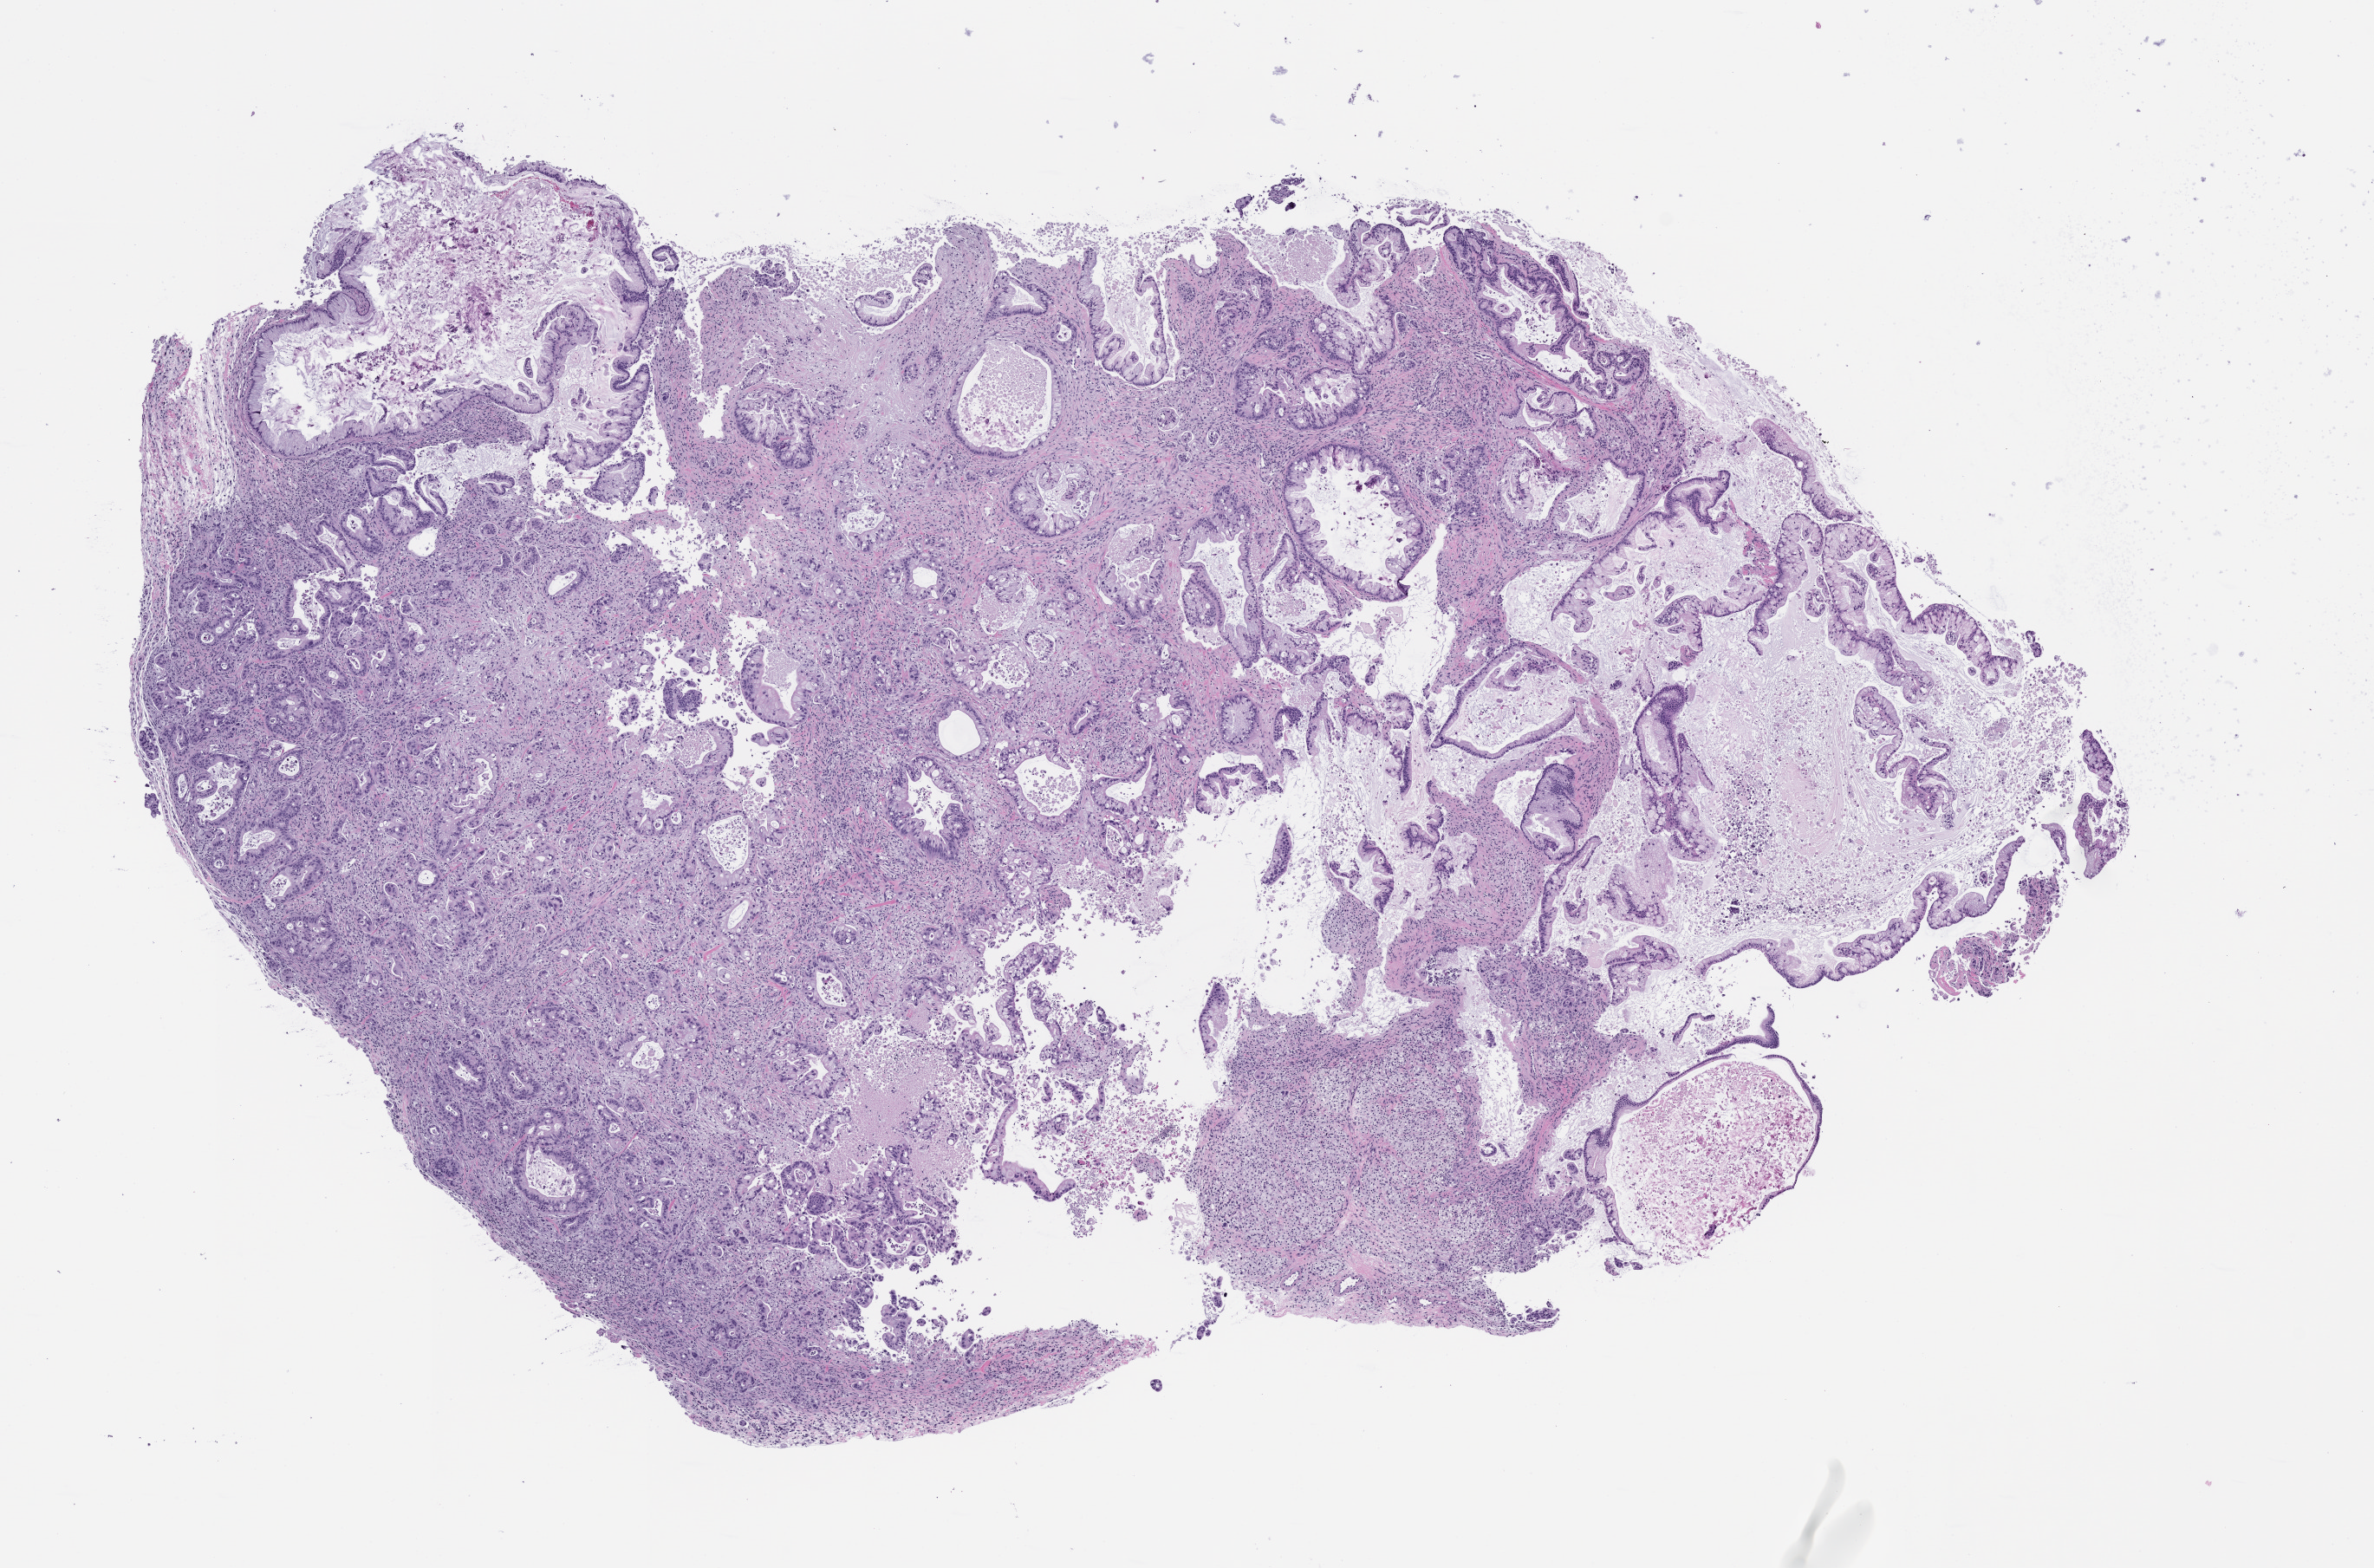
H&E whole-slide image of a patient-derived xenograft (PDX) tumor grown in a mouse, passage 0, low-resolution overview of the scanned area, about 11.0 x 7.3 mm. Formalin-fixed paraffin-embedded section. Tumor site category: pancreas.
* originating patient diagnosis: Pancreatic Adenocarcinoma